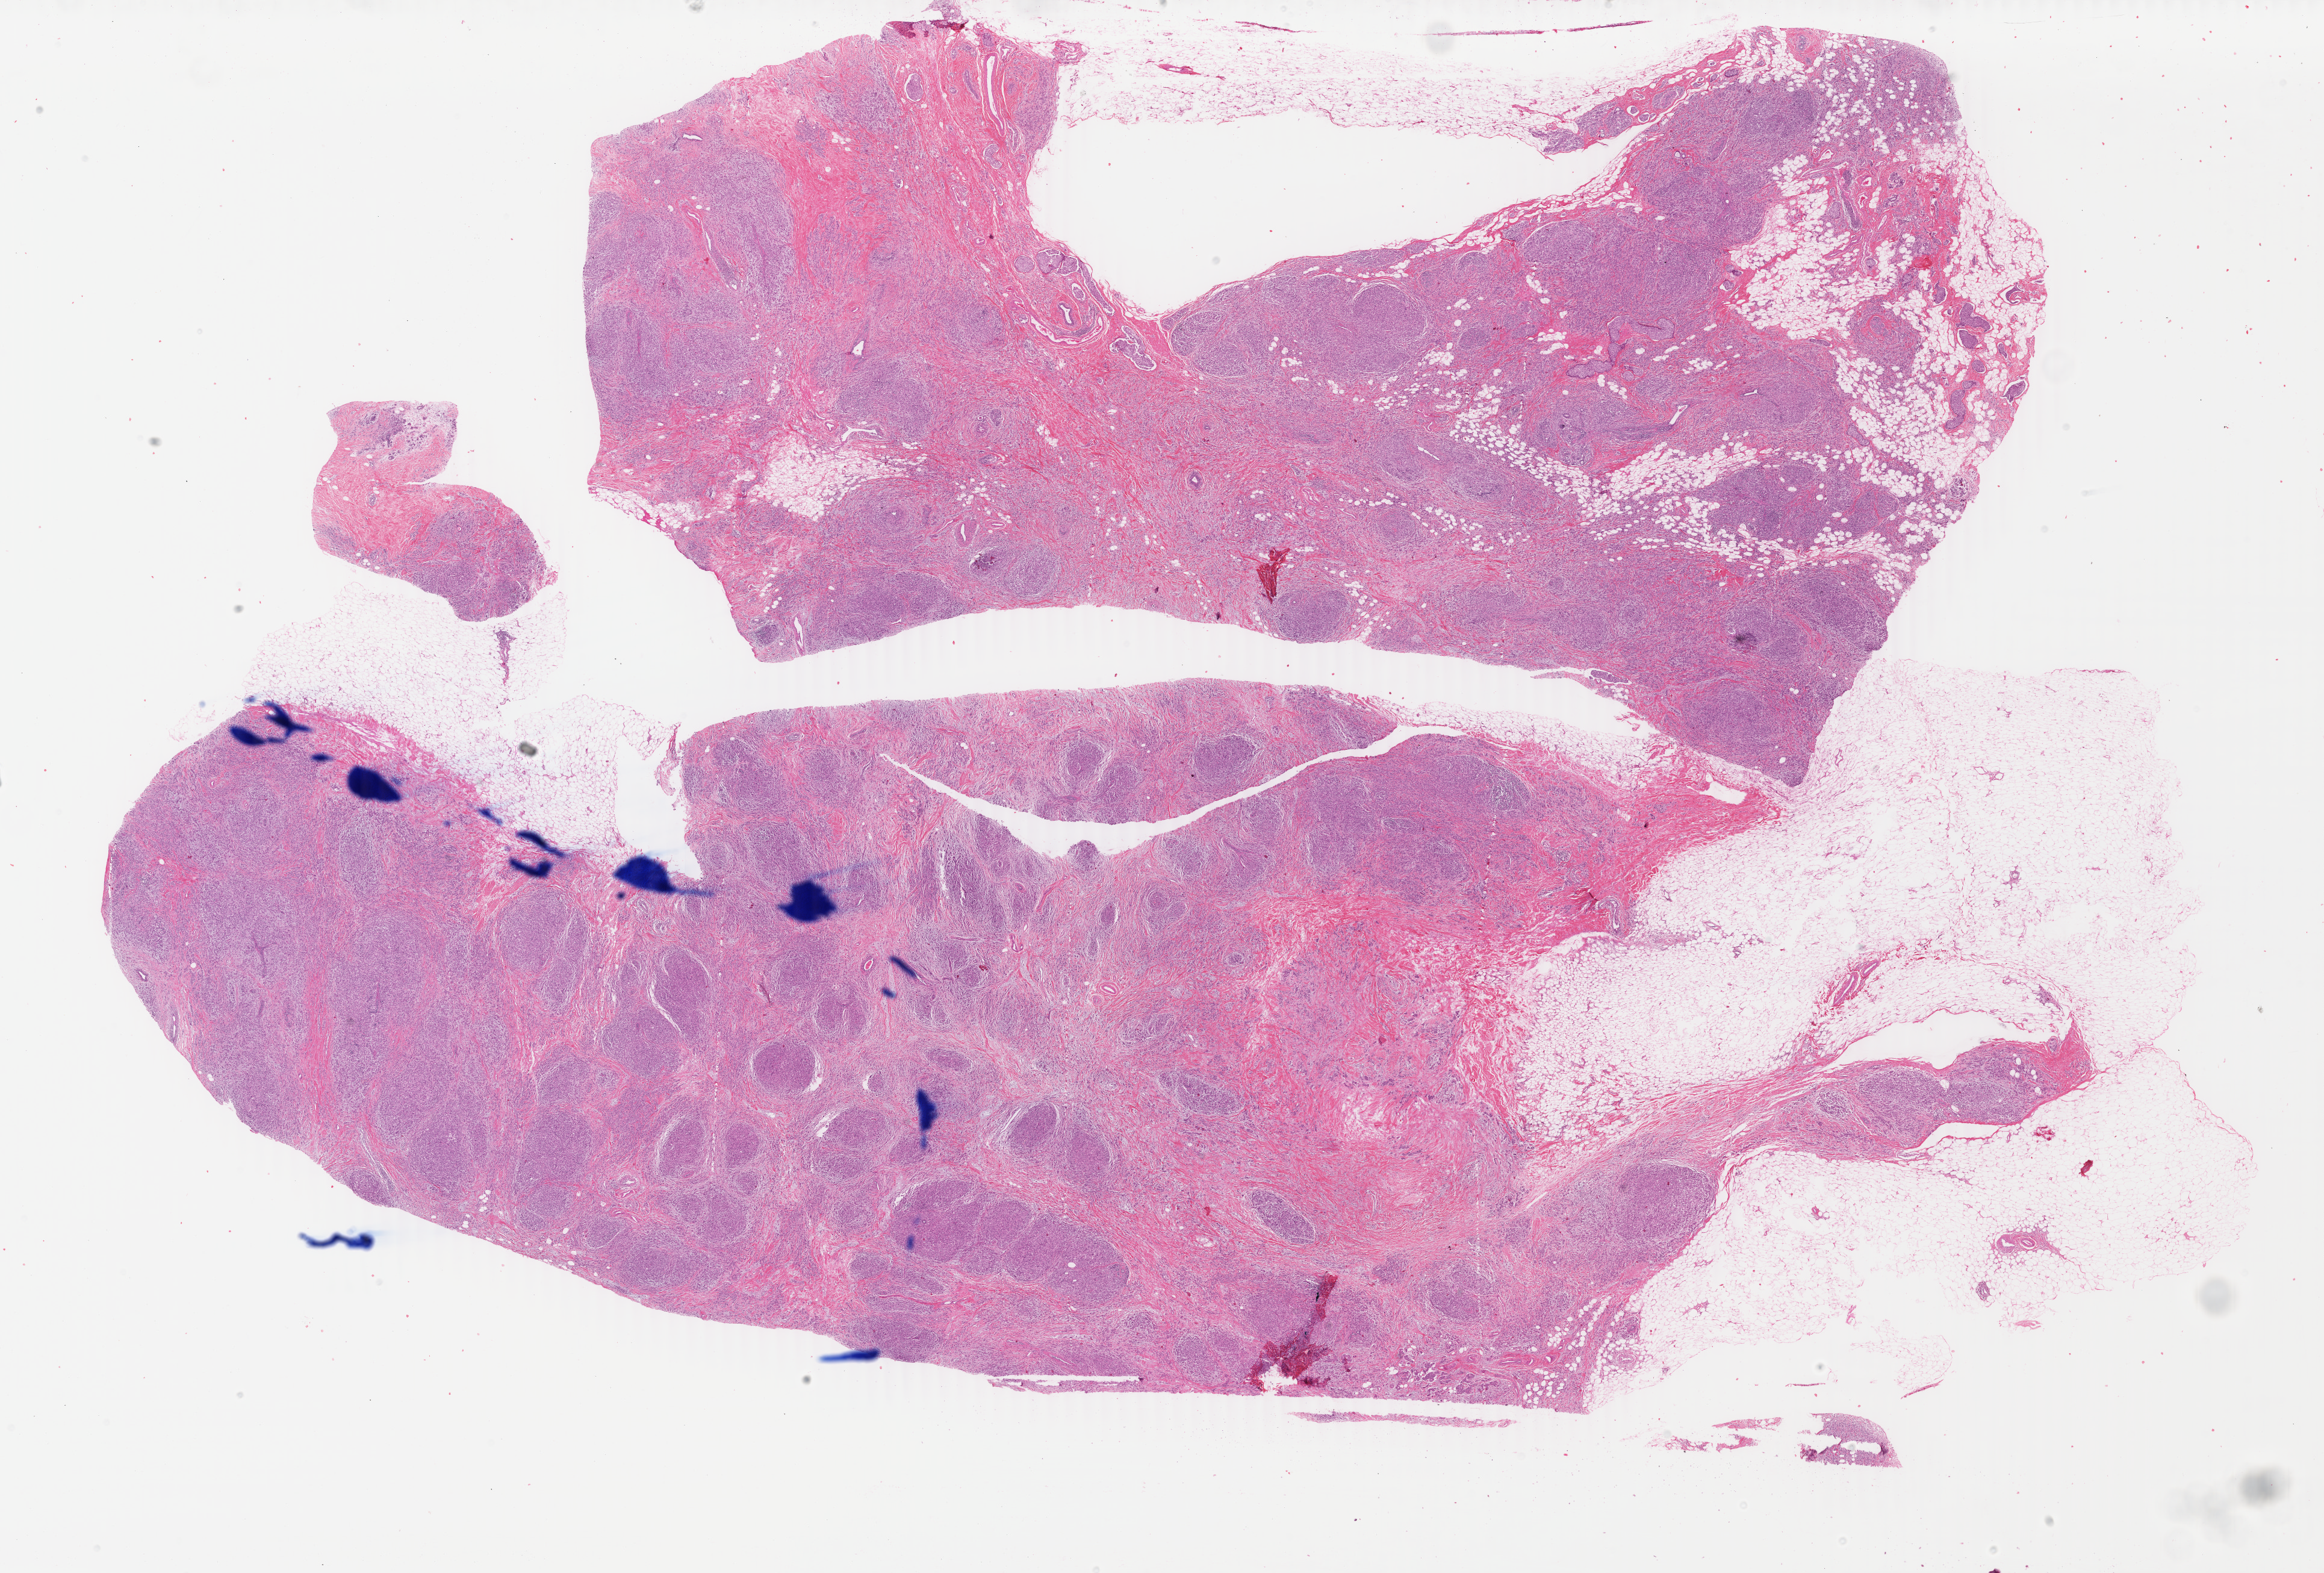
H&E whole-slide image — whole scanned area (about 30.7 x 20.8 mm, acquisition: 40x scan) shown as a low-resolution overview, FFPE section, primary tumour sample from the breast. Patient: female, age at initial diagnosis 38 years.
Histologic diagnosis: Lobular carcinoma, NOS.